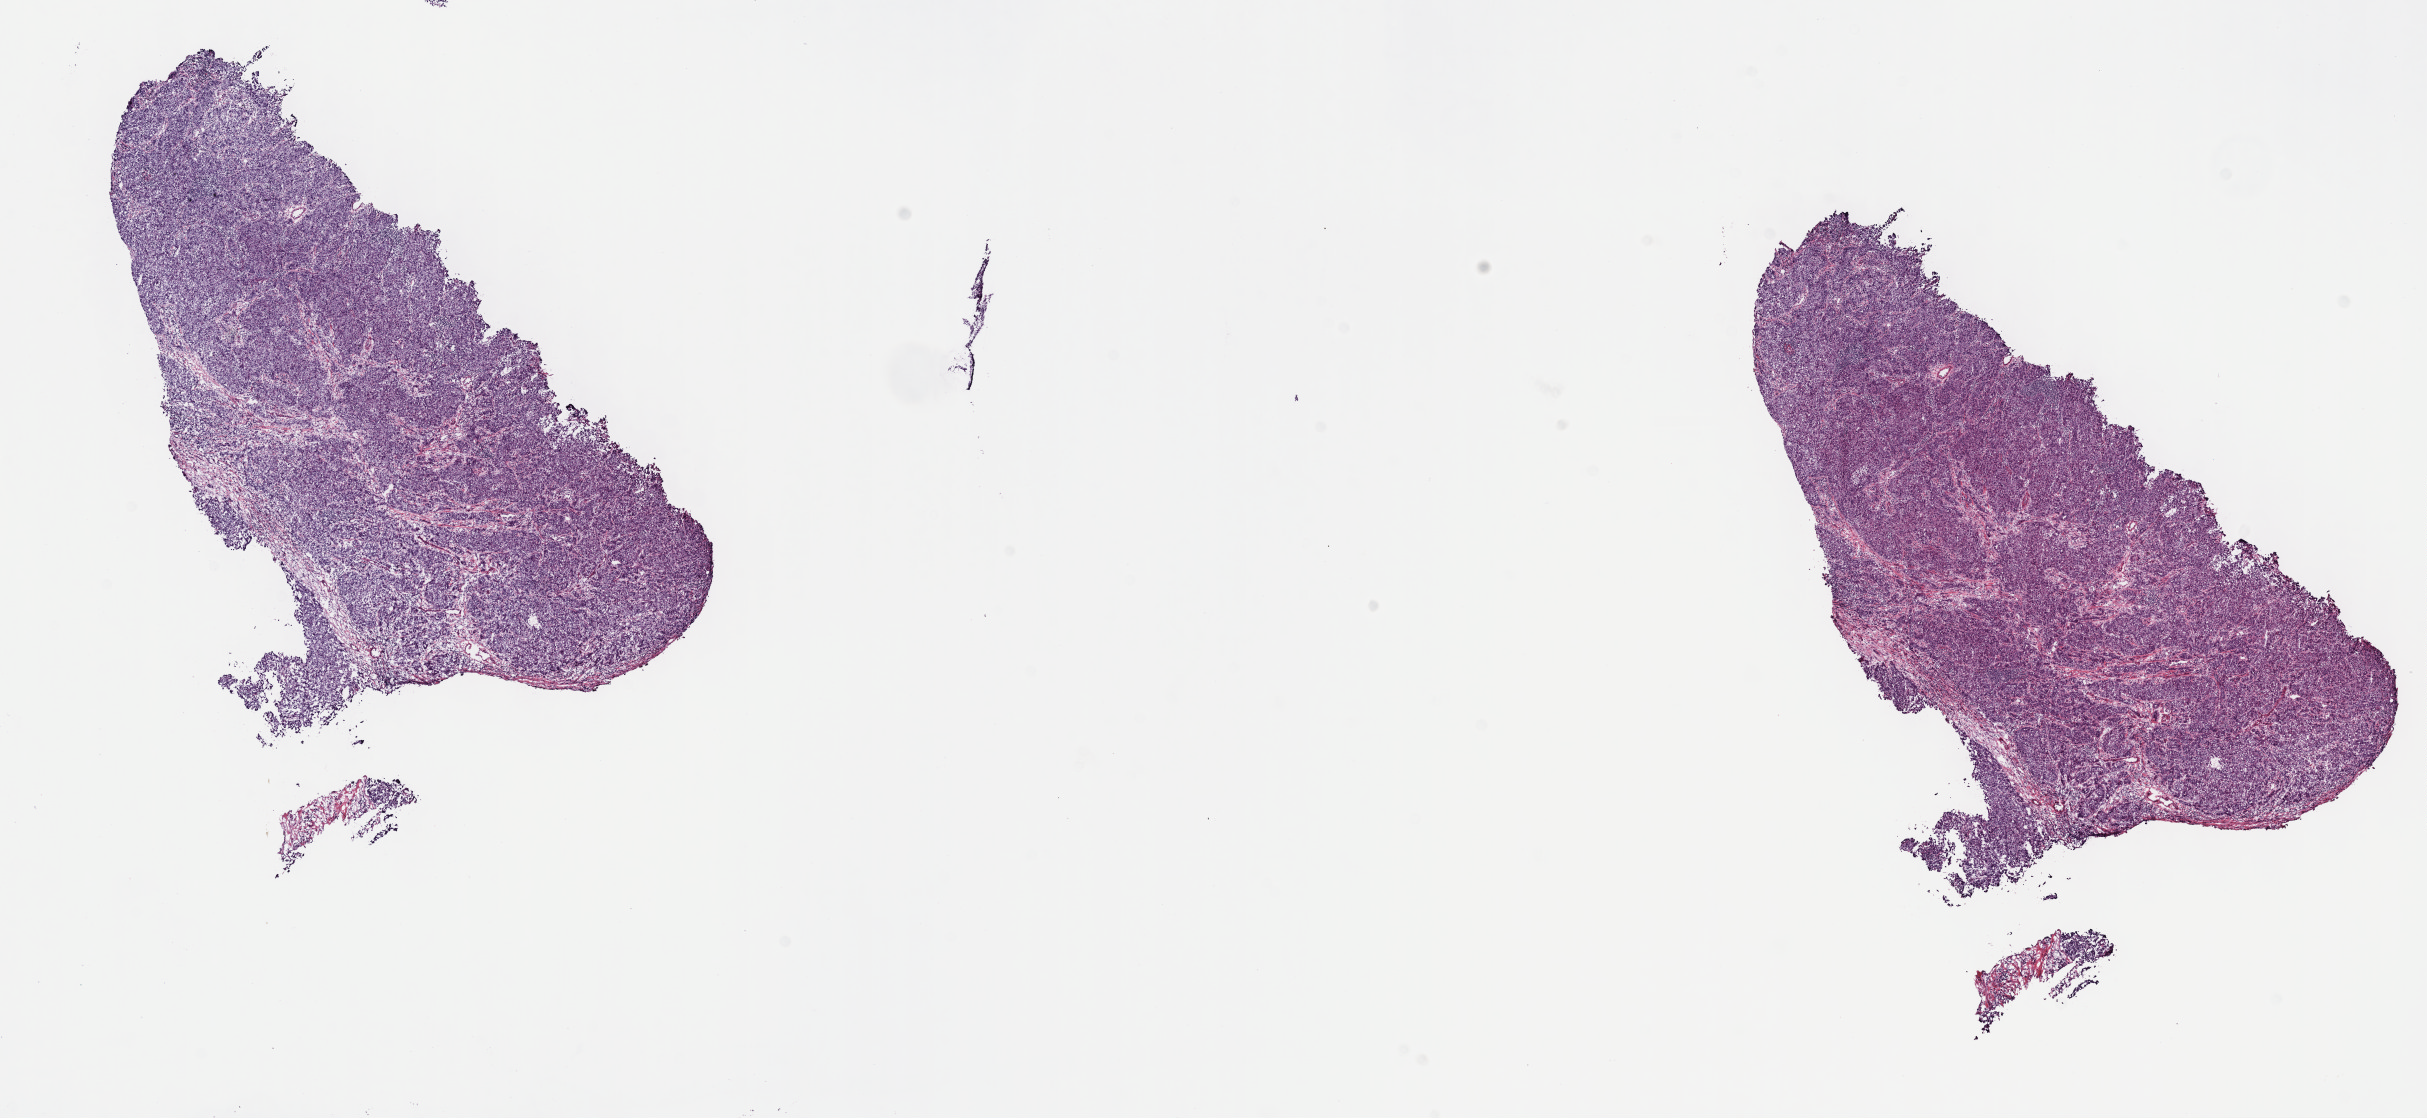
Whole-slide histology image, Hematoxylin and eosin (H&E) stained — whole scanned area (about 19.6 x 9.0 mm) shown as a low-resolution overview. Frozen section from the top of the tissue portion. Liver, primary tumour sample. Patient: male, age at initial diagnosis 38 years. Histologic grade: G2 (moderately differentiated). Slide review estimates, as recorded: tumour cells 75%, tumour nuclei 75%, normal cells 0%, stromal cells 24%, necrosis 1%. Inflammatory infiltration, as recorded: lymphocyte infiltration 3%, monocyte infiltration 1%, neutrophil infiltration 4%.
• AJCC pathologic stage: I
• diagnosis: Hepatocellular carcinoma, NOS
• TNM: T1 N0 M0